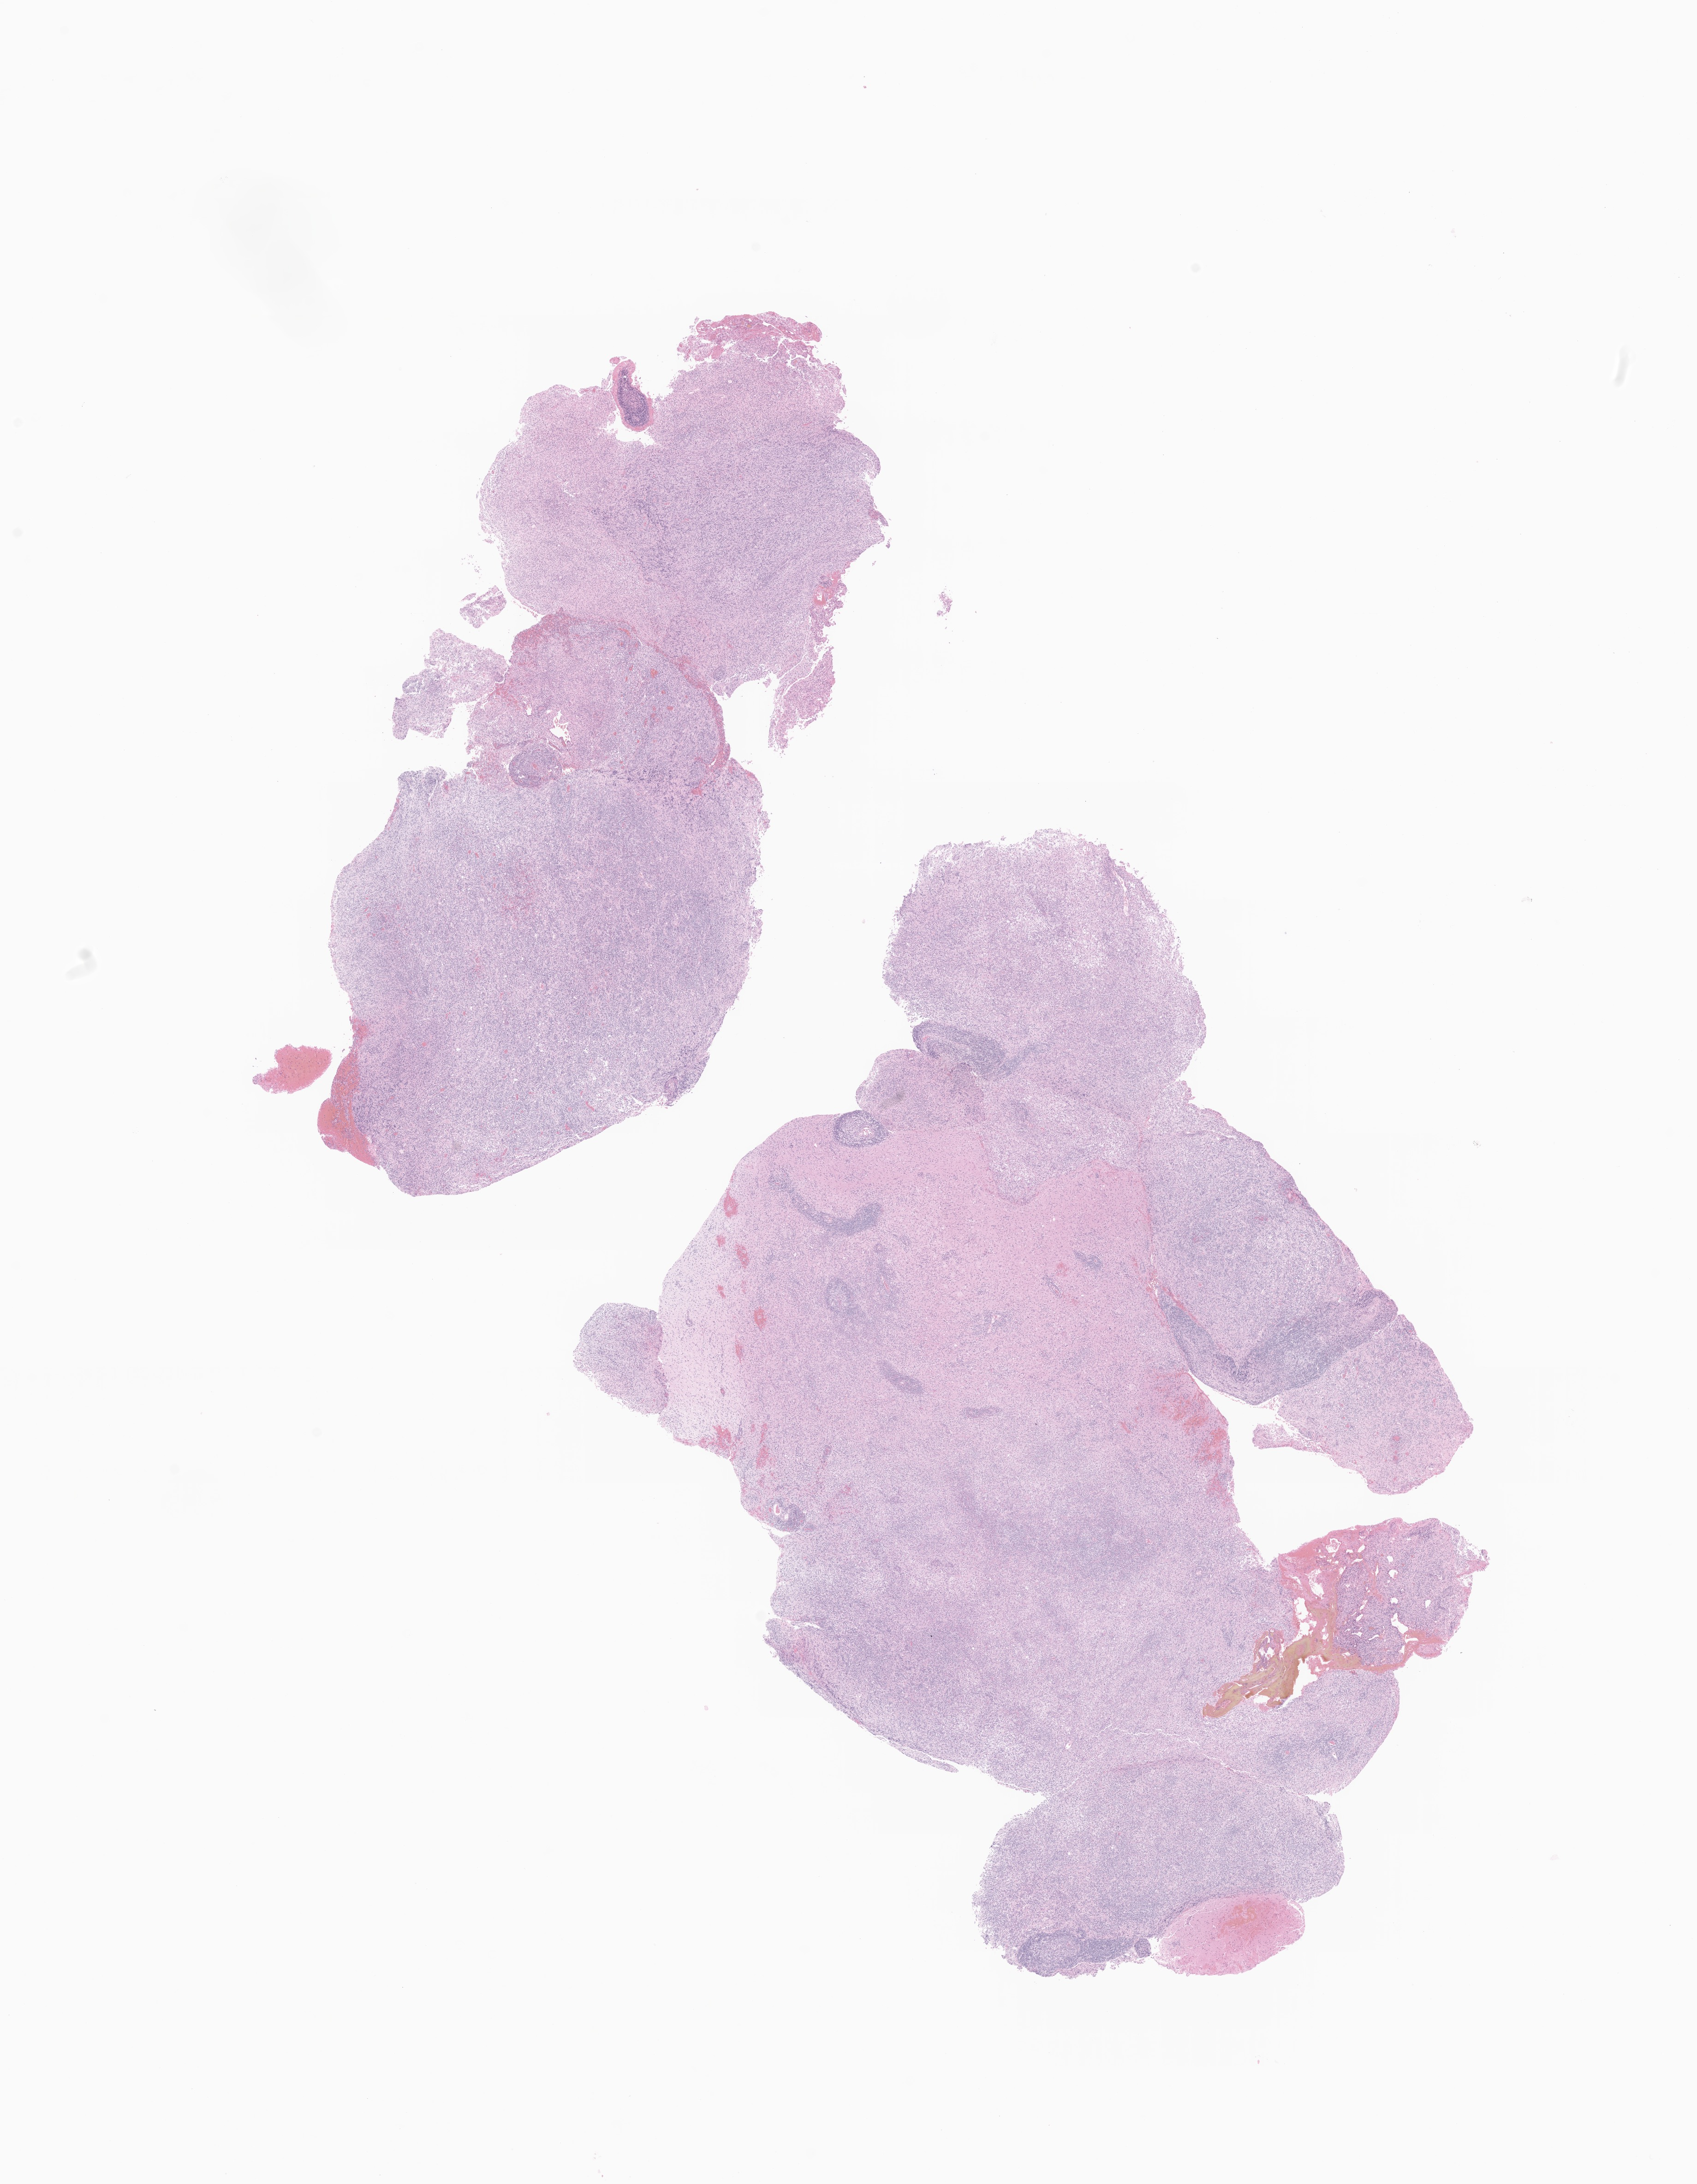
Whole-slide image, H&E stain of tumor tissue from the brain — a low-resolution overview of the entire scanned area, about 15.5 x 20.0 mm. FFPE section. Patient: male, age 94 months (7 years 10 months).
Recorded diagnosis: Glioma, malignant.